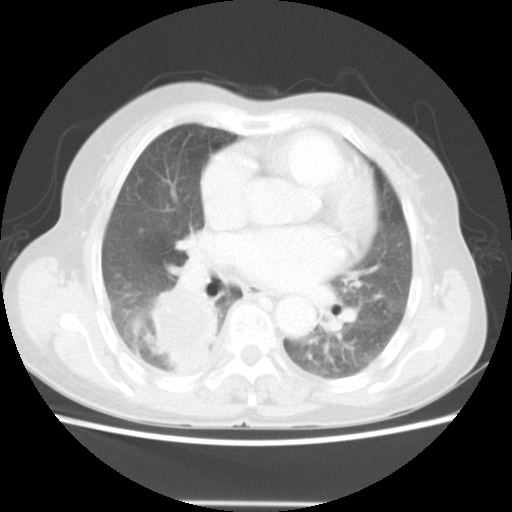
Chest CT, one axial slice. Slice 26 of 52 in the series (ordered by position). Reconstruction kernel STANDARD. 140 kVp. Lung window (W 1500 / L -600 HU). 512 × 512 image matrix, field of view 337 × 337 mm. Patient: female, 67 years. Case-level facts recorded for this patient, not image findings: clinical TNM (as recorded): T3 N1 M1.
Structures marked on this image (bounding box drawn by a radiologist):
- lung tumour (recorded histology: adenocarcinoma): bounding box [x1, y1, x2, y2] px = [142, 285, 222, 378]